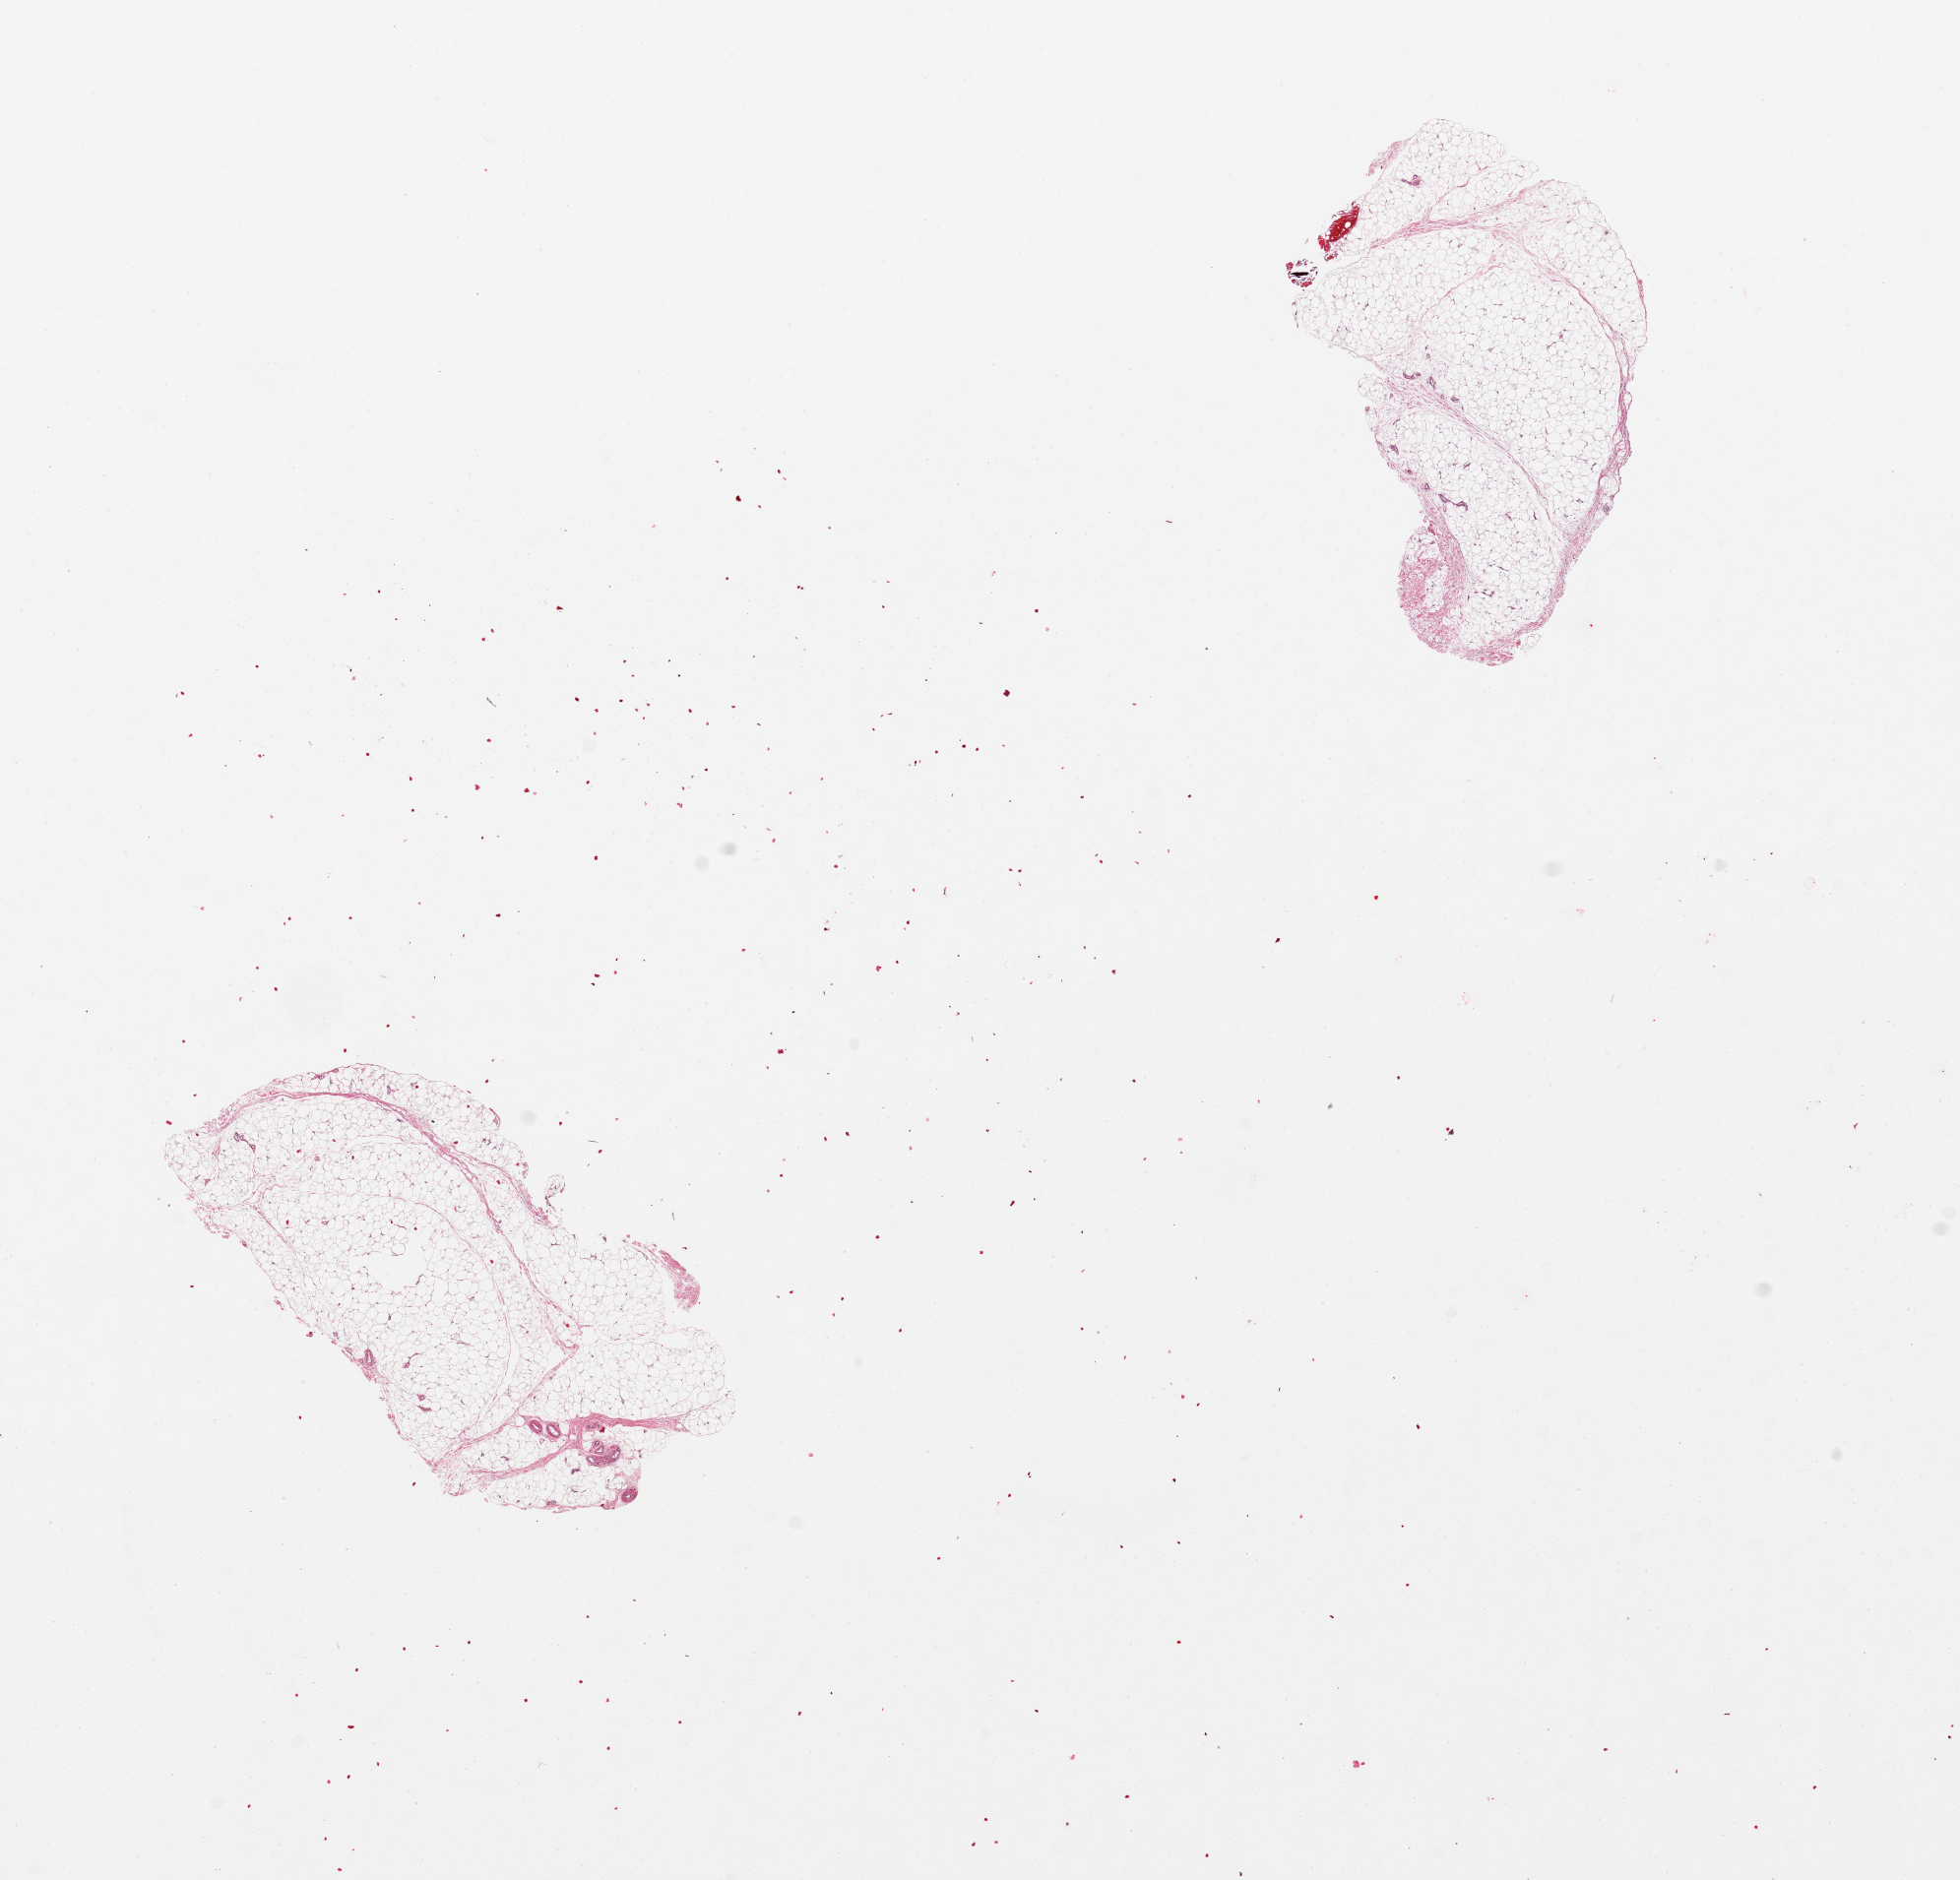
Hematoxylin and eosin (H&E) whole-slide image — shown as a low-resolution overview of the whole scanned area (about 15.8 x 15.1 mm, acquisition: 20x scan), PAXgene-fixed paraffin-embedded (PFPE) section, sampled site (target tissue): tibial nerve, donor tissue sample. Donor: male.
Pathologist's review note for this sample: 2 pieces. NO NERVE; all adipose.